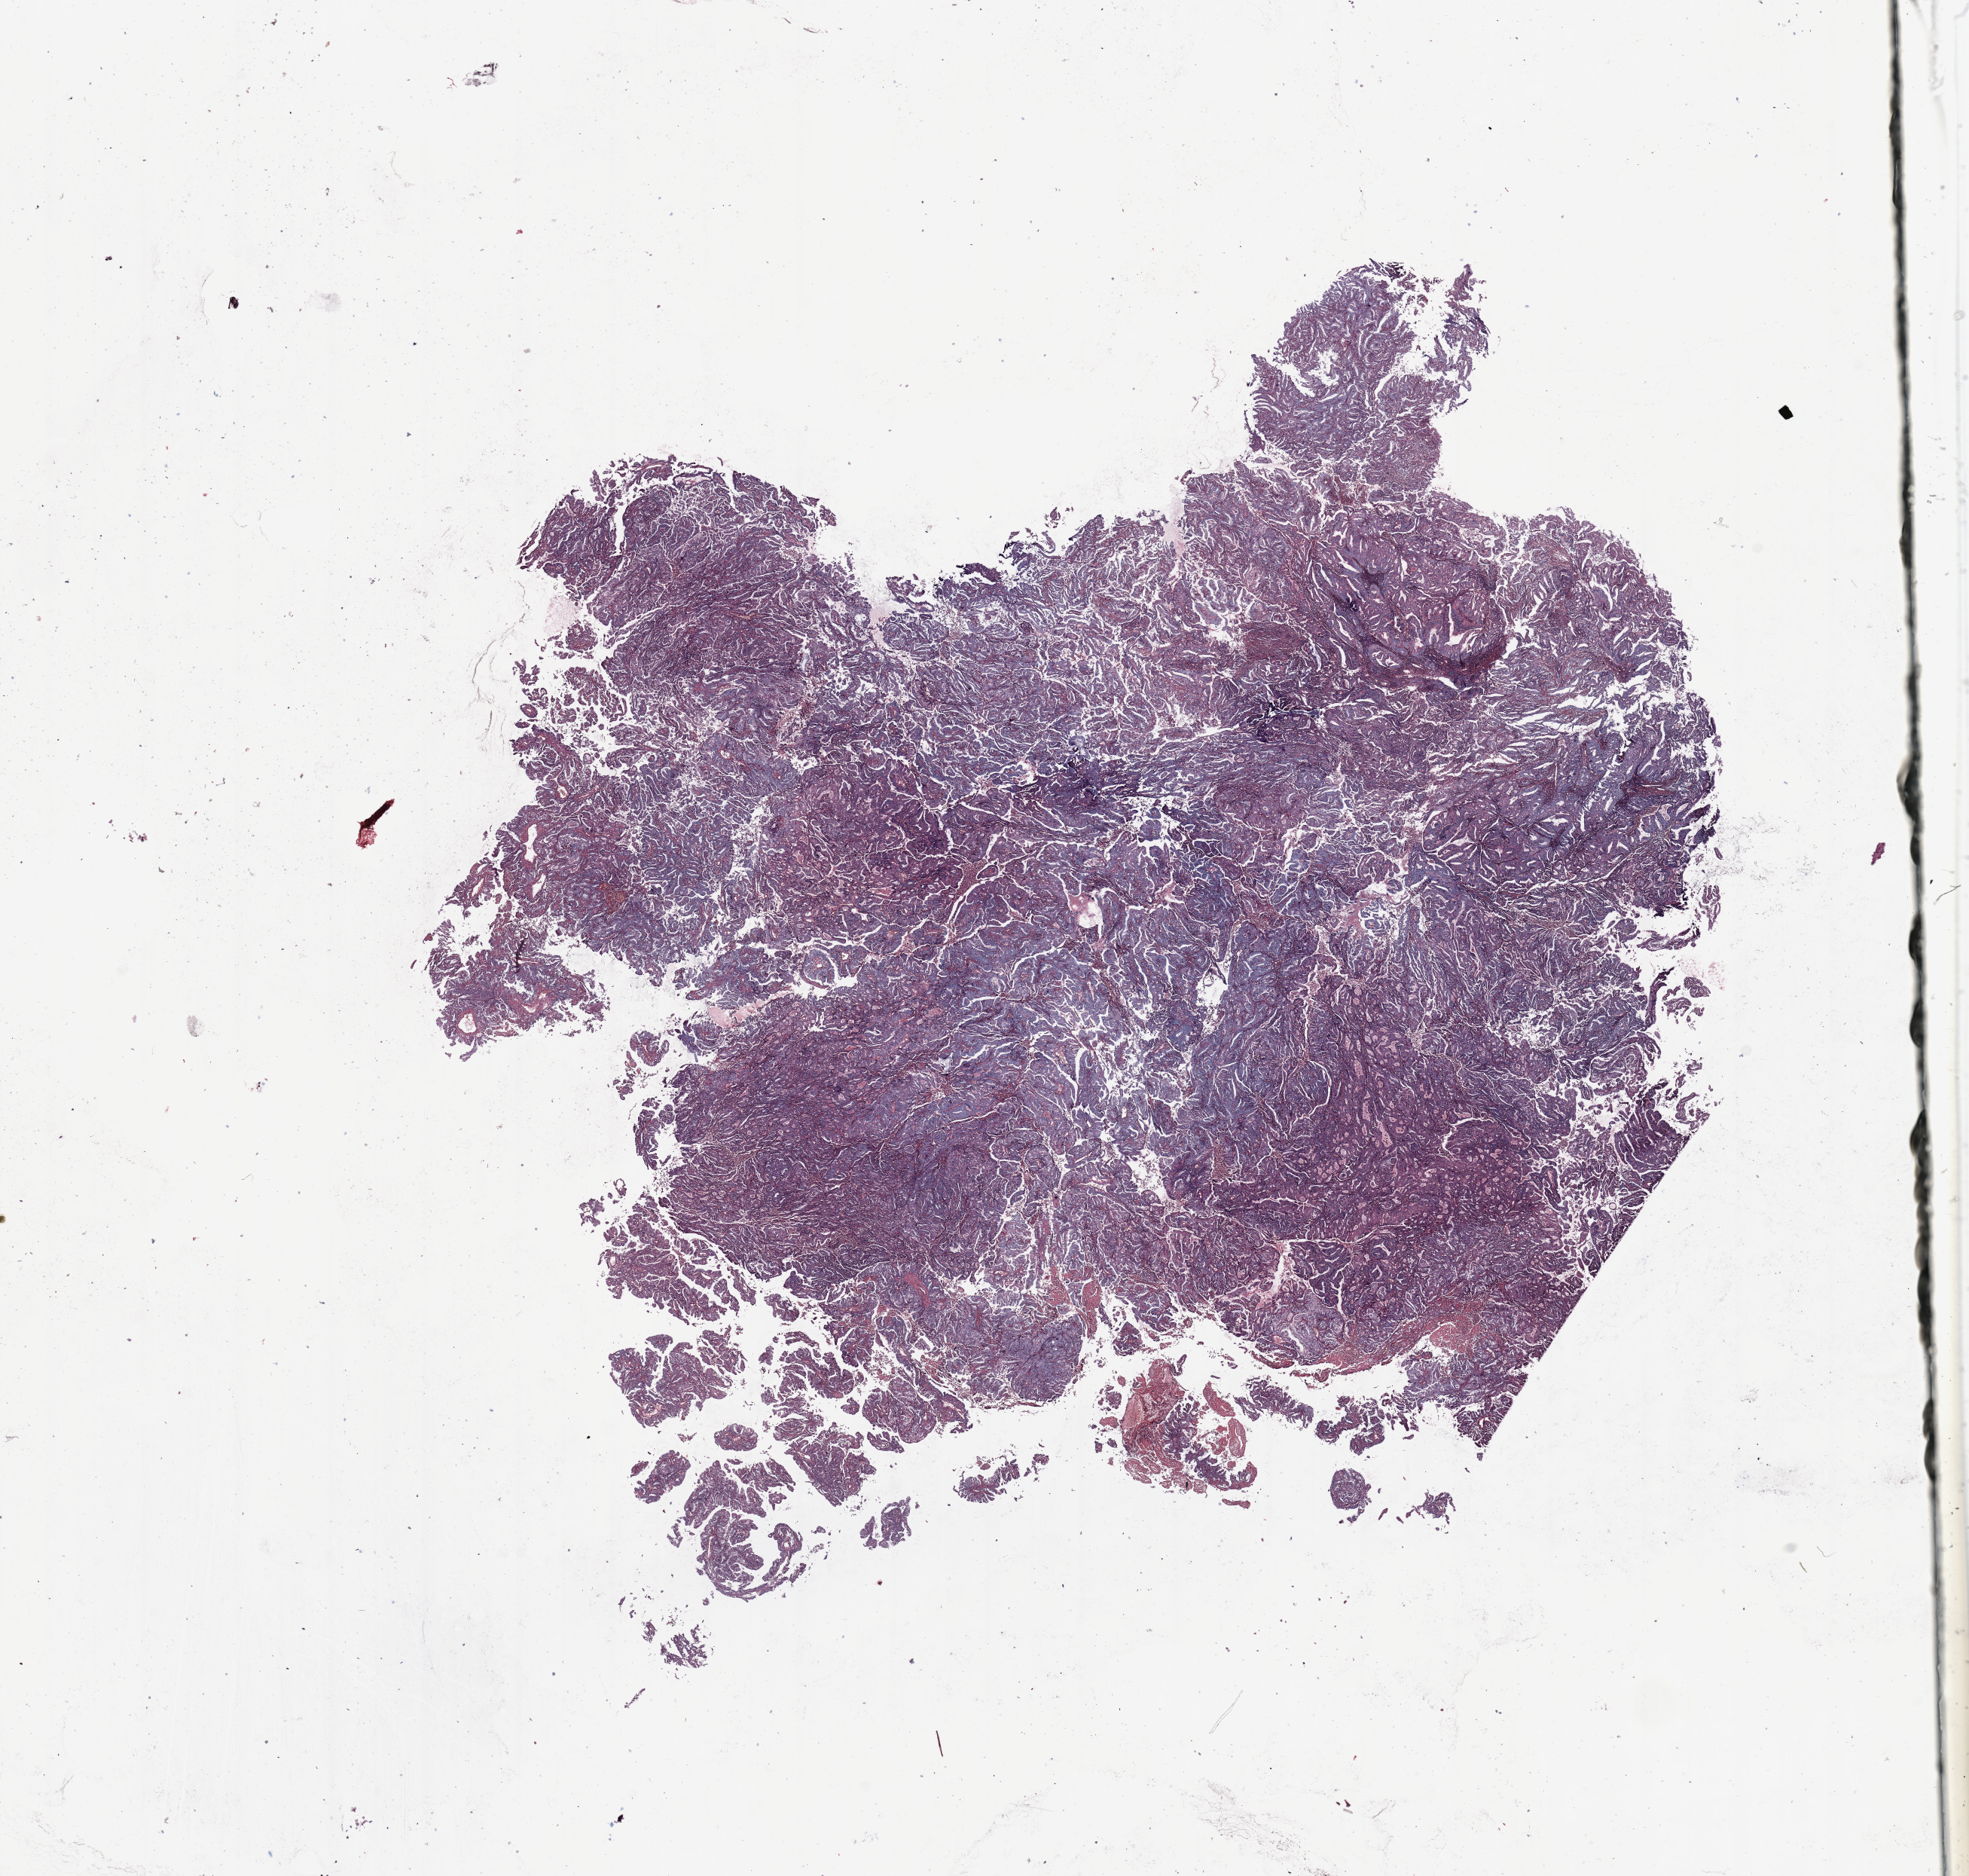
Whole-slide histology image, H&E — shown as a low-resolution overview of the whole scanned area (about 20.7 x 19.7 mm). Uterus, tumour tissue. 63-year-old female patient.
Histologic diagnosis: Endometrioid adenocarcinoma, NOS.